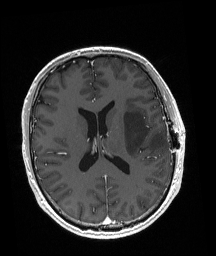
Brain MRI from a brain-tumour surgery series, one axial slice. Position 85 of 192 along the scan axis. T1-weighted post-contrast. 1 mm slice thickness. 216 × 256 image matrix. From the clinical record (not read from this slice): histopathology: Astrocytoma; WHO grade: 3; IDH mutation: yes.
Structures marked on this image (expert manual segmentation):
- tumour: box from (x=123, y=110) to (x=167, y=157) px